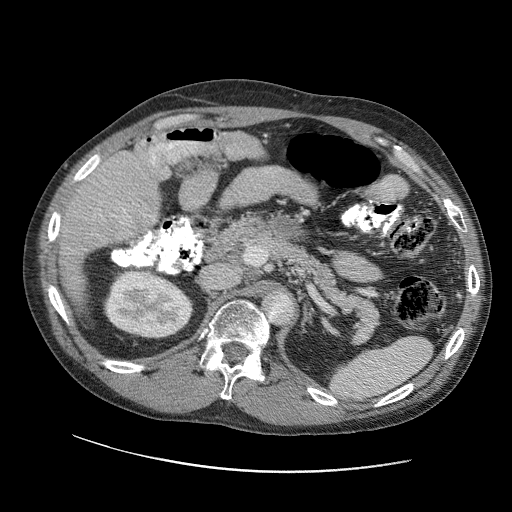
Contrast-enhanced abdominal CT (liver protocol), one axial slice. Position 57 of 109 along the scan axis. 120 kVp. Soft-tissue window (W 400 / L 40 HU). 2.5 mm slice thickness. 512 × 512 image matrix, field of view 400 × 400 mm. From the clinical record (not read from this slice): diagnosis: hepatocellular carcinoma (patient treated with transarterial chemoembolisation; whether this scan precedes or follows treatment is not stated here); TNM stage (as recorded): Stage-IIIC; Child-Pugh class: B; tumour differentiation: well differentiated; tumour nodularity: uninodular.
Annotated regions visible in this slice (semi-automatically segmented with operator editing):
- liver parenchyma outside the tumour (the mass and vessels are separate outlines, so this box may not span the whole liver): box from (x=56, y=136) to (x=232, y=304) px
- liver vessels: (x=110, y=136)–(x=227, y=225)